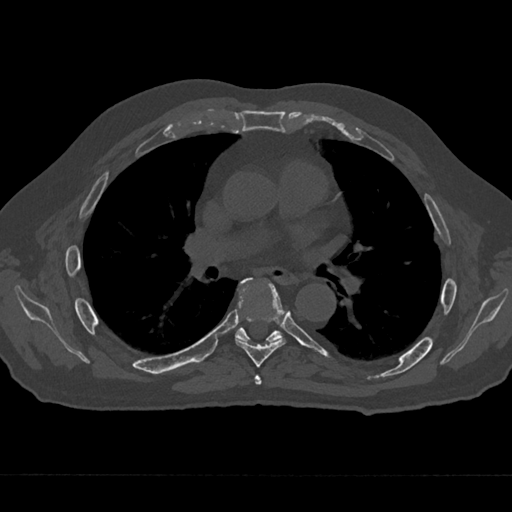
CT including the spine, one axial slice; slice 403 of 797 in the series (ordered by position); 120 kVp; bone window (W 1800 / L 400 HU); 0.5 mm slice thickness; 512 × 512 image matrix, field of view 377 × 377 mm. Patient: male, 75 years. From the clinical record (not read from this slice): primary cancer: renal.
Outlined on this slice (semi-automatic segmentation, software-assisted and operator-edited):
- T5 vertebra: bounding box [x1, y1, x2, y2] px = [255, 375, 262, 385]
- T6 vertebra: [235, 278, 286, 368]
- T7 vertebra: [235, 279, 283, 343]